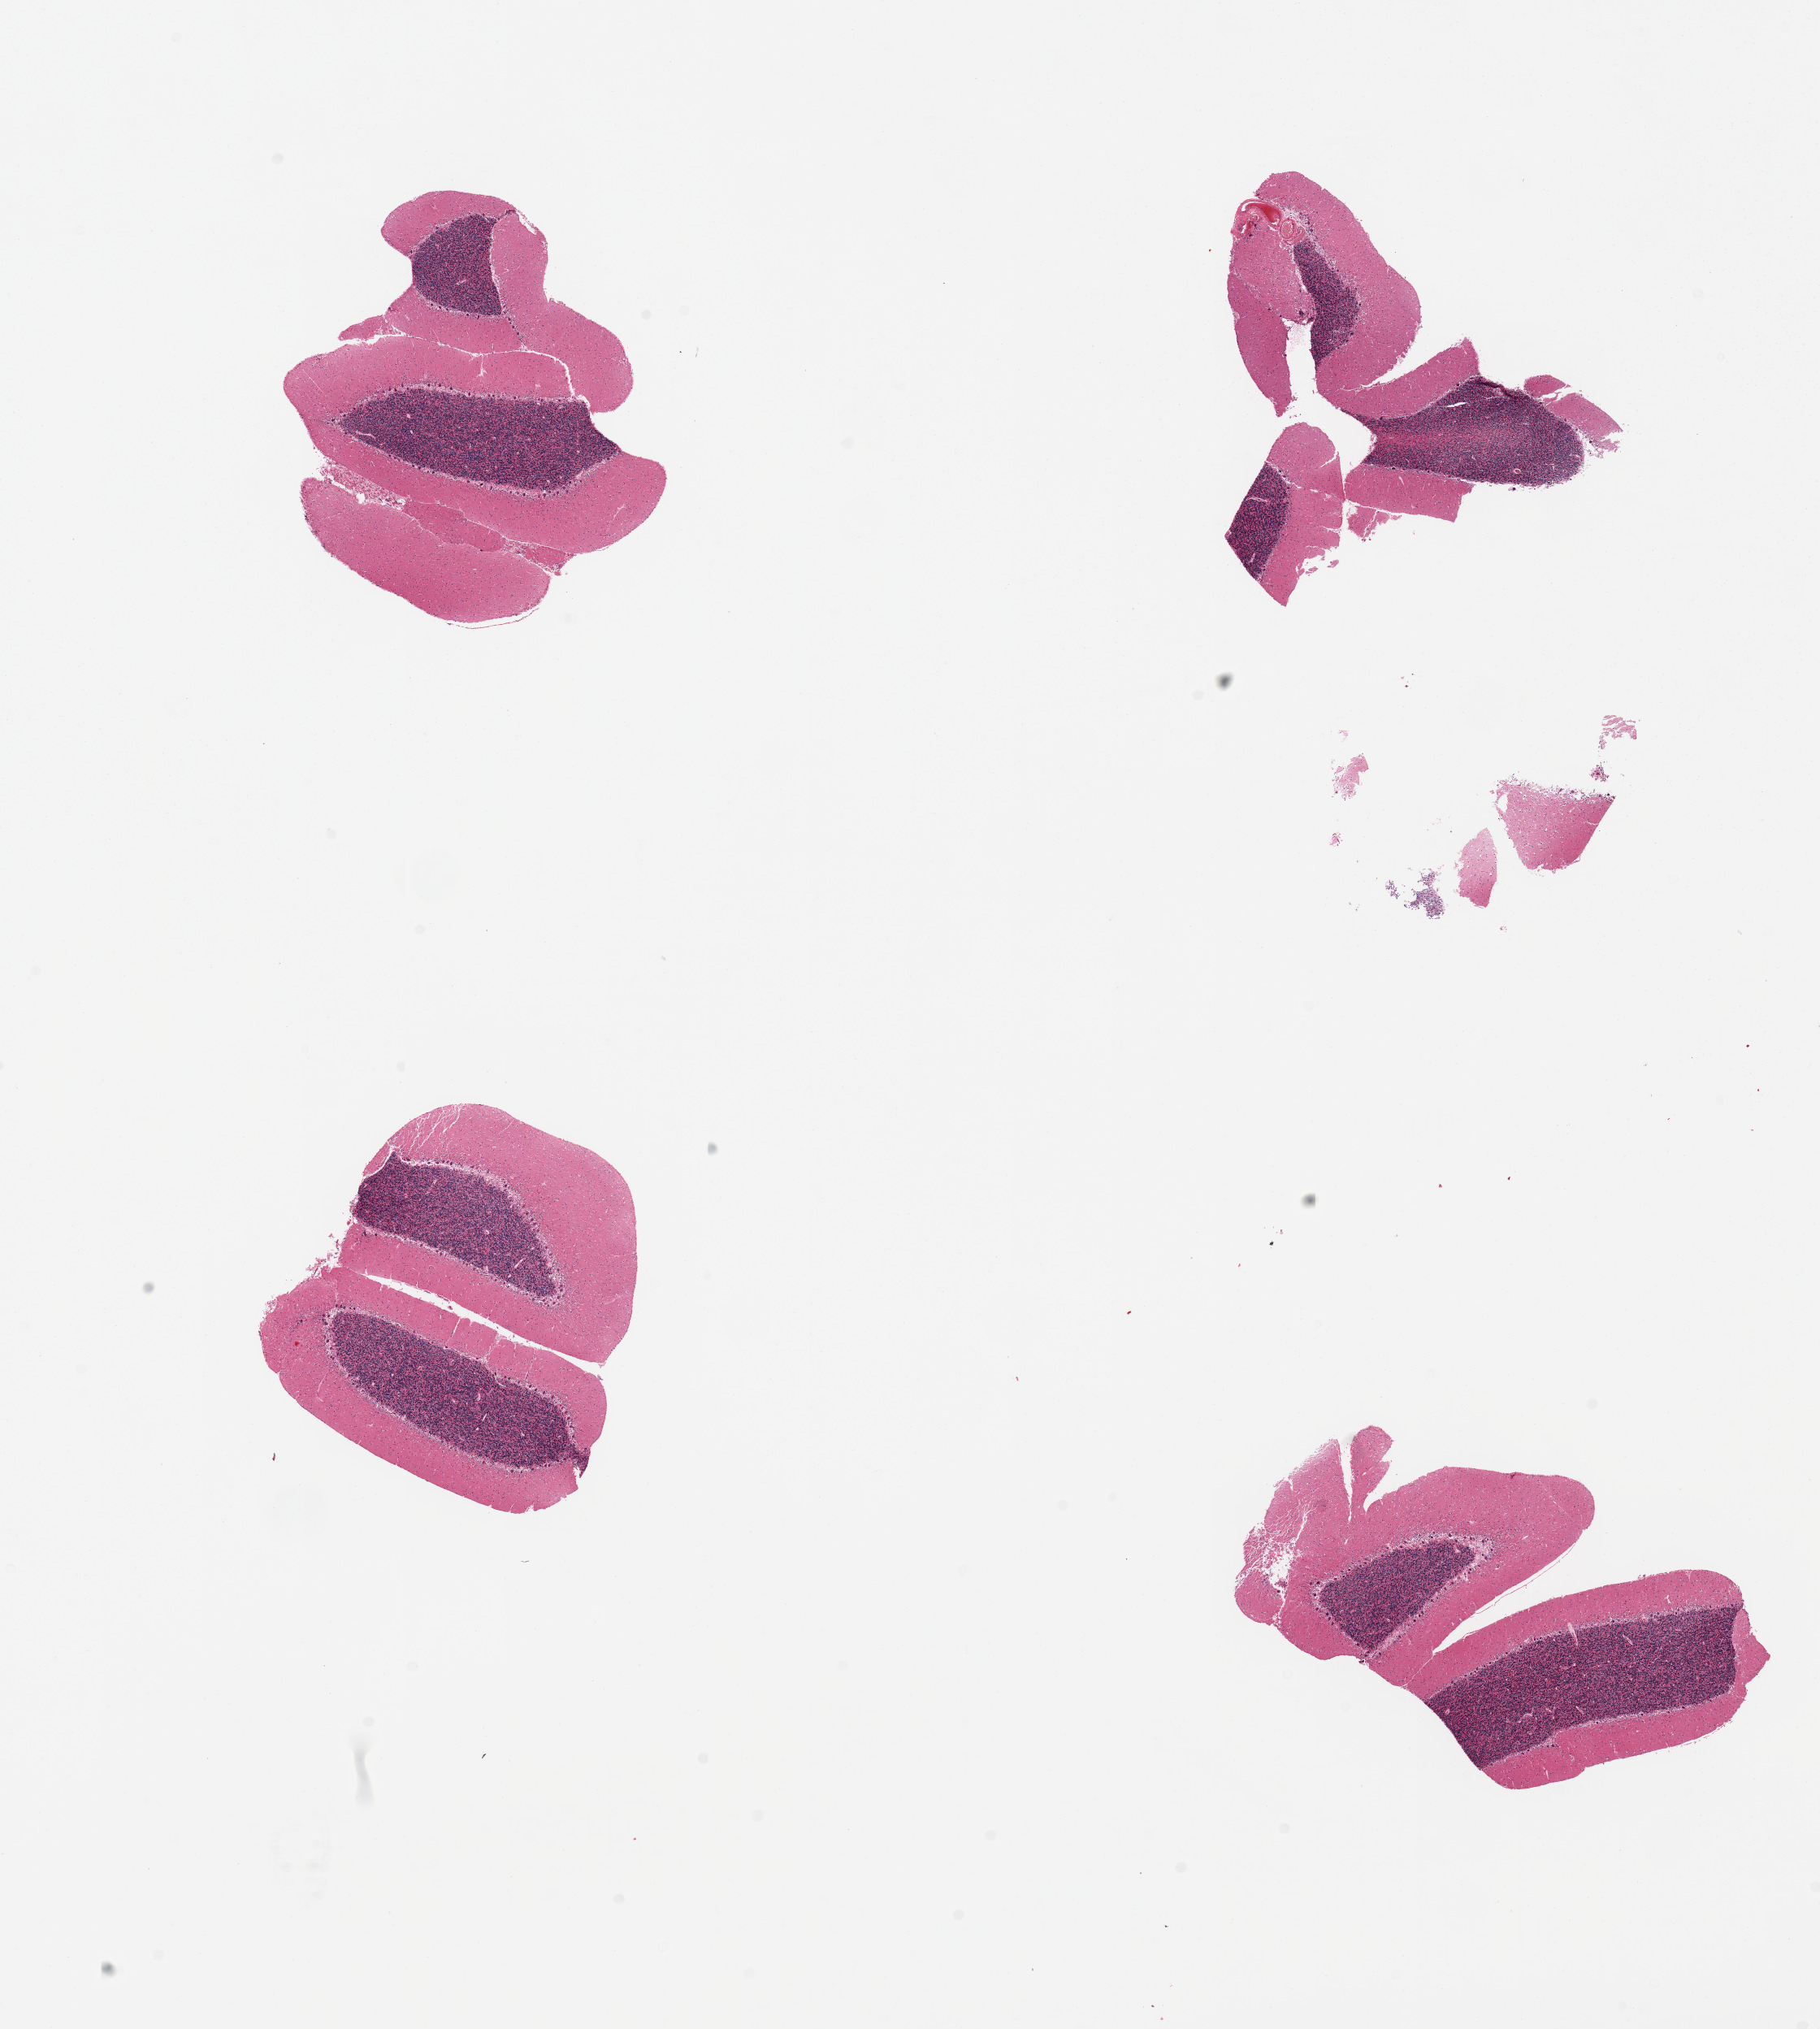
H&E whole-slide image, shown as a low-resolution overview of the whole scanned area (about 17.7 x 19.8 mm). PAXgene-fixed paraffin-embedded (PFPE) section. Sampled site (target tissue): cerebellum. Donor tissue sample. Male donor.
- review note (as recorded): 4 pieces